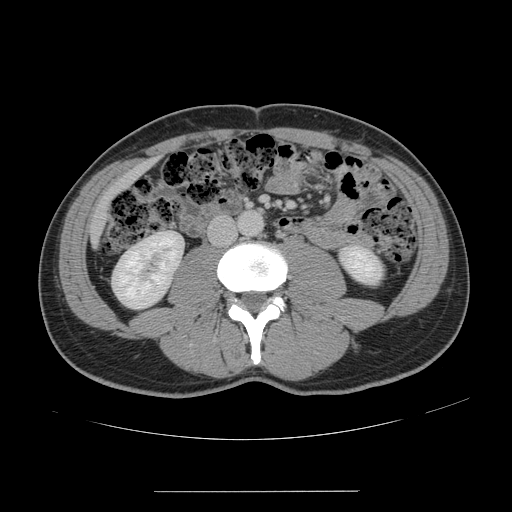
Contrast-enhanced abdominal CT, one axial slice; position 29 of 178 along the scan axis; intravenous contrast given; soft-tissue window (W 400 / L 40 HU); 512 × 512 image matrix, field of view 401 × 401 mm. Male patient, age 53 years. From the clinical record (not read from this slice): diagnosis: colorectal cancer liver metastases, imaged before liver resection; multiple liver metastases: yes; largest metastasis: 2.4 cm; disease in both lobes: no.
Outlined on this slice (expert manual segmentation):
- liver: bounding box <93,163,150,241> (left, top, right, bottom; pixels)